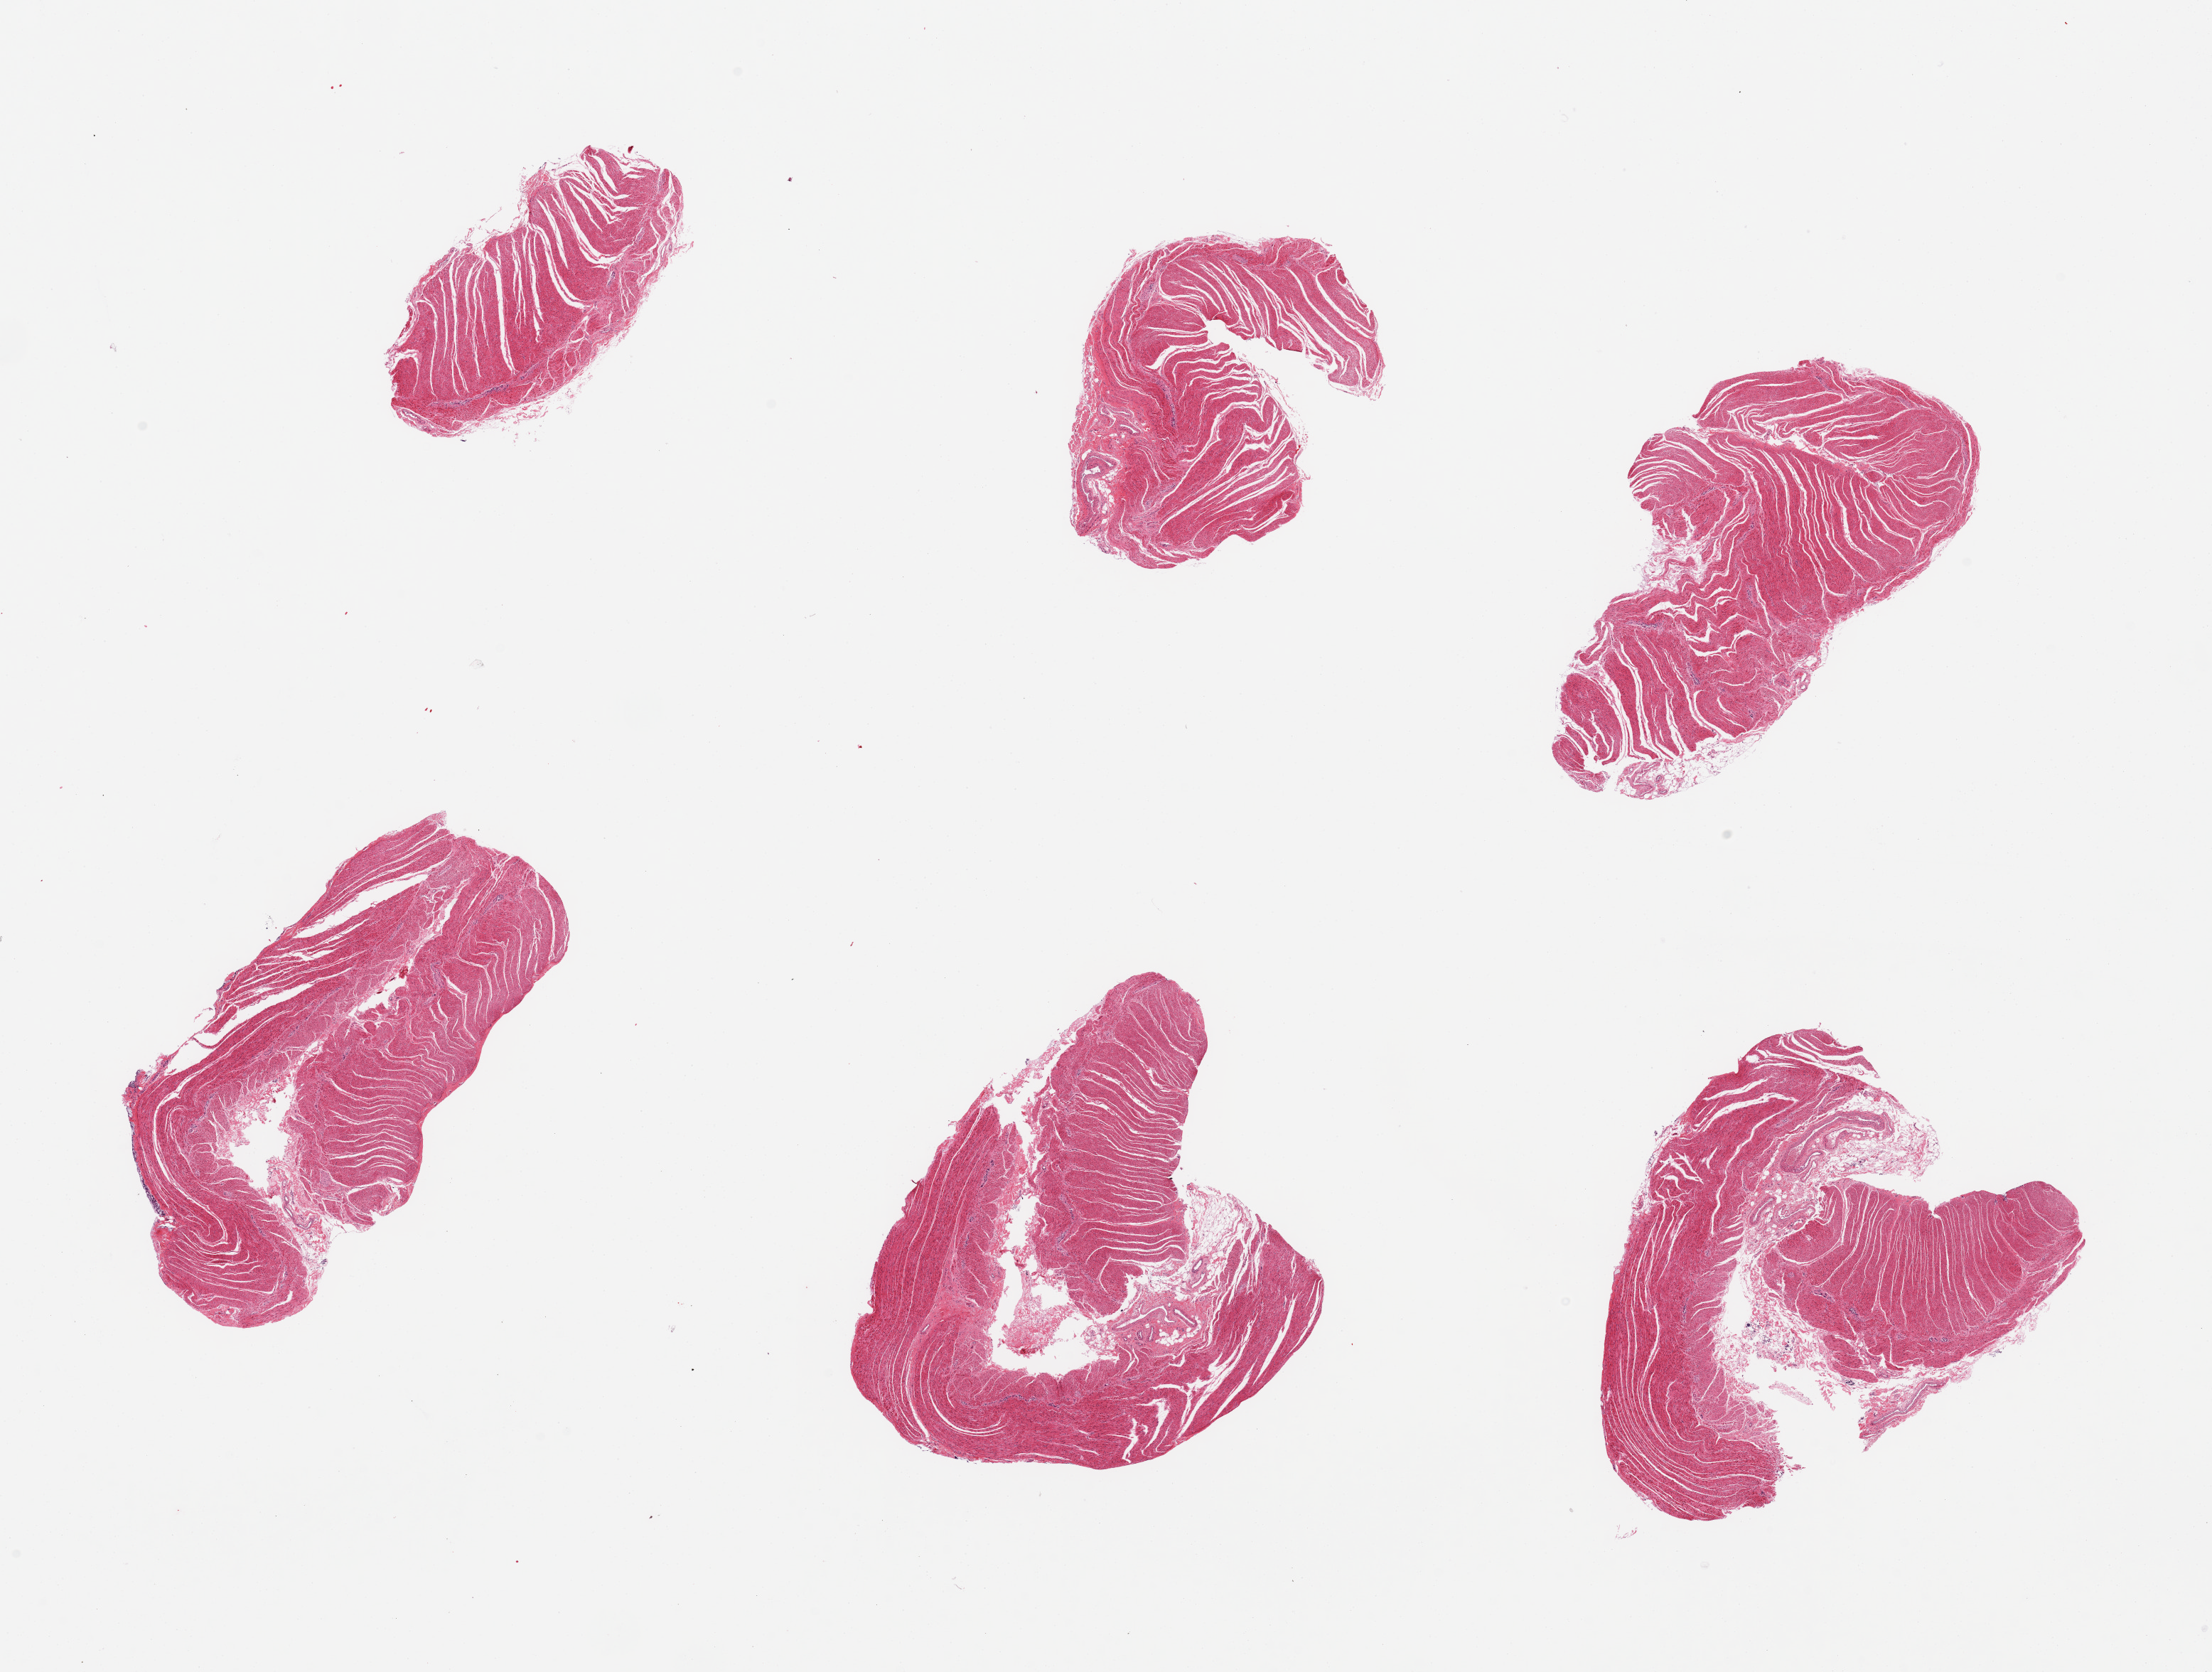
Digitized H&E-stained section, brightfield — a low-resolution overview of the entire scanned area, about 24.6 x 18.6 mm; PAXgene-fixed, paraffin-embedded tissue; target tissue: sigmoid colon; donor tissue sample. Female donor.
Review note (as recorded): 6 pieces; well dissected muscle.